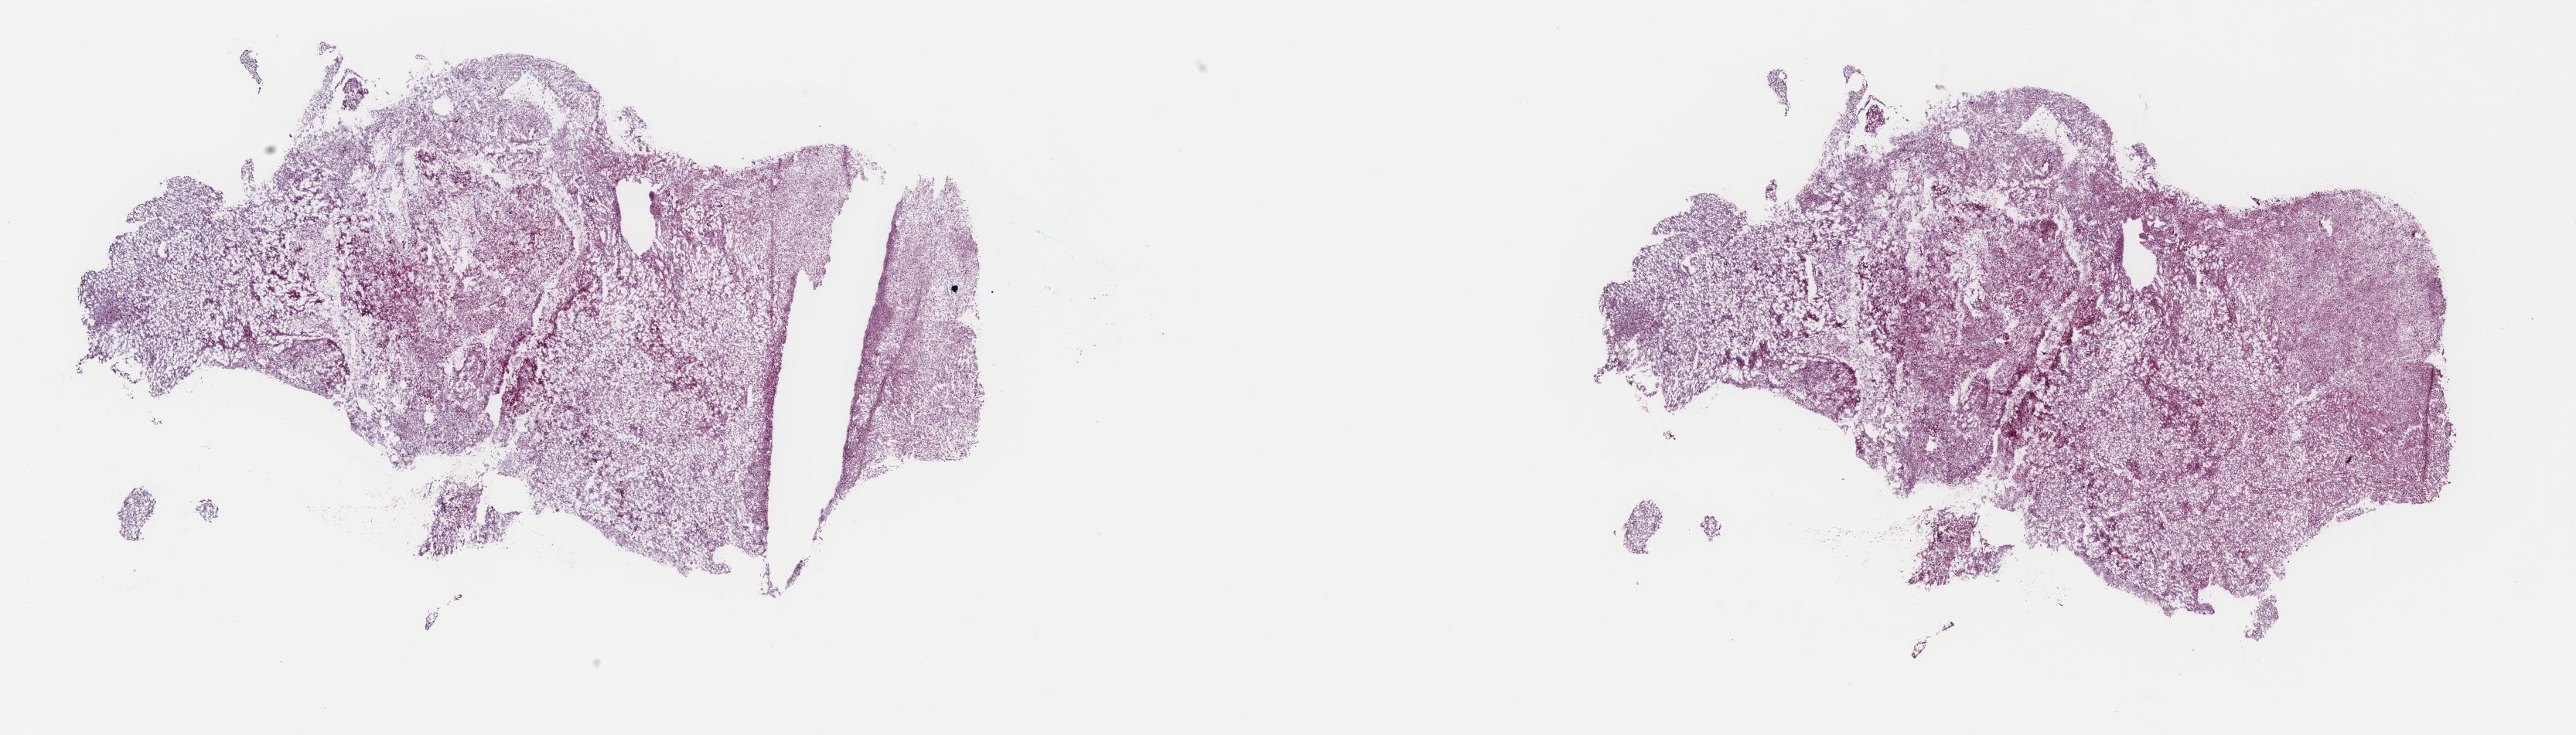
Digitized H&E tissue section (whole slide), low-resolution overview of the scanned area, about 26.4 x 7.5 mm; frozen section; brain, primary tumour sample. Female, age 52 years at initial diagnosis.
Histologic diagnosis: Astrocytoma, anaplastic (cerebrum).